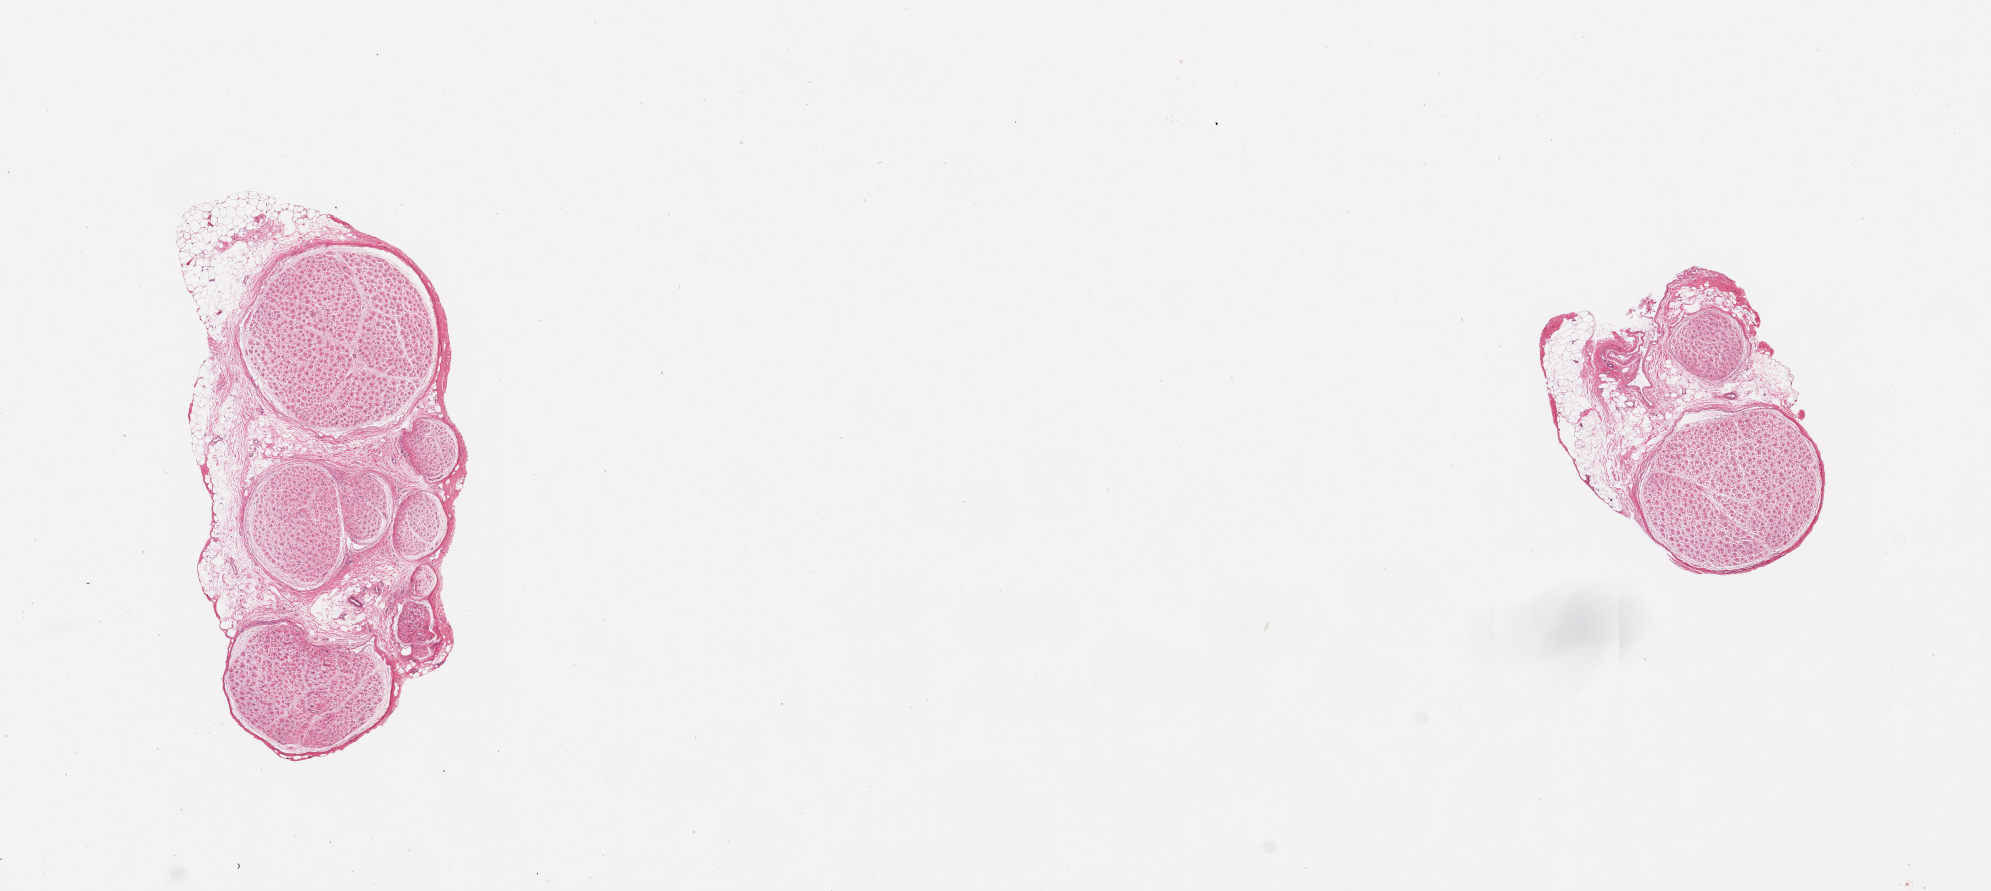
Digitized hematoxylin and eosin (H&E)-stained section, brightfield, low-resolution overview of the scanned area, about 15.8 x 7.0 mm; PAXgene-fixed, paraffin-embedded tissue; target tissue: tibial nerve; tissue donor sample. Female donor.
- pathologist's review note for this sample: 2 pieces, 2x1.5mm & 2x4mm; ~20% adjacent adipose